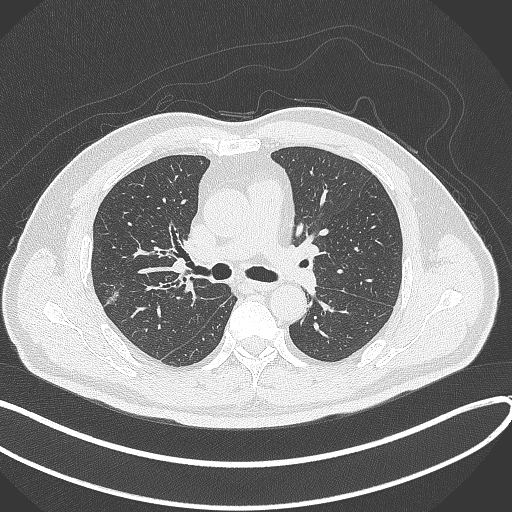
Chest CT, one axial slice; reconstruction kernel B70f; lung window (W 1500 / L -600 HU); 1 mm slice thickness; 512 × 512 image matrix. Patient: male, 60 years. From the clinical record (not read from this slice): clinical TNM (as recorded): T1c N0 M0.
Structures marked on this image (rectangle marked by the reading radiologist):
- lung tumour (recorded histology: adenocarcinoma): bounding box <98,278,124,311> (left, top, right, bottom; pixels)